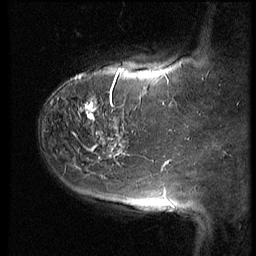
Breast MRI (dynamic contrast-enhanced), one sagittal slice; slice 14 of 64 in the series (ordered by position); 3 images stored at this slice position (order not interpretable as contrast timing); 1.5 T; TE 4.2 ms, TR 9 ms; 2.5 mm slice thickness; 256 × 256 image matrix, field of view 180 × 180 mm. Female patient, age 59 years. From the clinical record (not read from this slice): setting: breast cancer imaged before/during neoadjuvant chemotherapy; receptor status: HER2-positive.
Structures marked on this image (semi-automatic segmentation, software-assisted and operator-edited):
- analysis volume of interest (the breast-tissue region the enhancement analysis was run in; not a lesion): bounding box (x1, y1, x2, y2) in pixels: (54, 65, 155, 132)
- tumour enhancement mask (voxels above the 140 % enhancement threshold inside the analysis volume of interest): (86, 99, 118, 129)